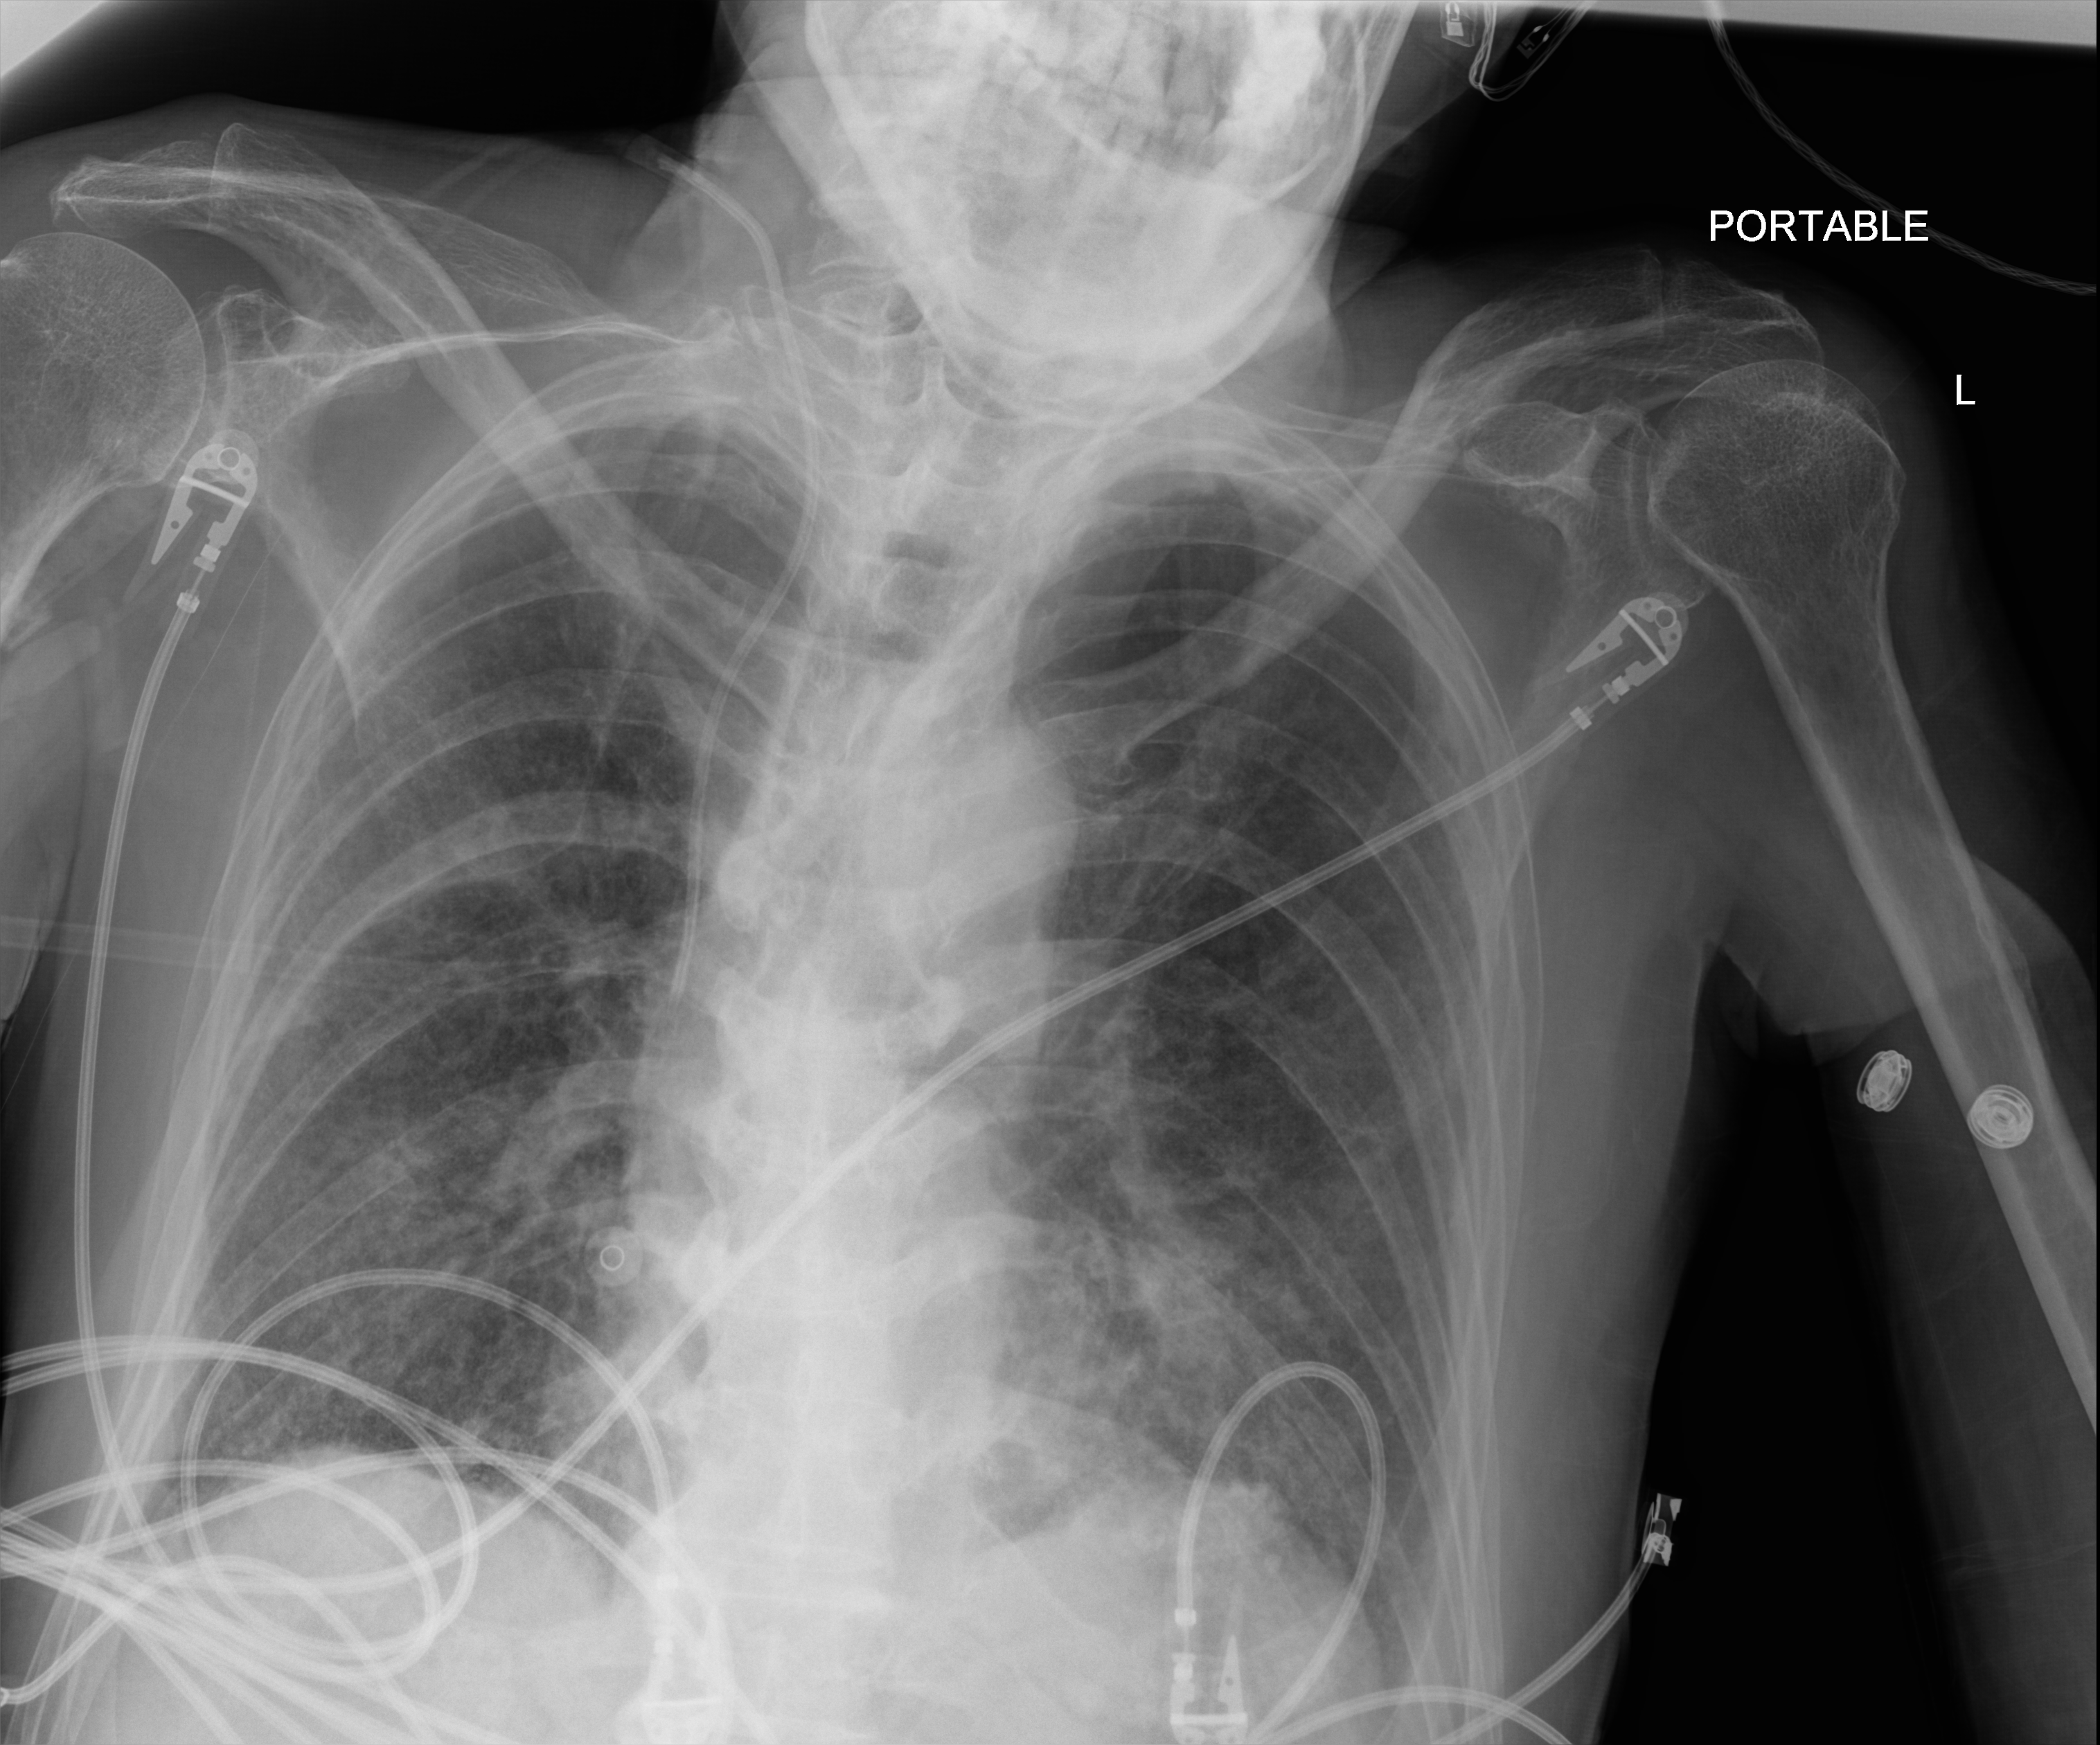
Portable chest radiograph; anteroposterior (AP) projection. Male patient hospitalised with COVID-19, age 60–74 years.
From the hospital-stay record, not from the radiograph (when in the stay this image was taken is not recorded): admitted to intensive care during this hospital stay: yes; length of hospital stay: 42 days.